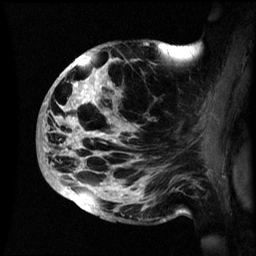
Breast MRI (dynamic contrast-enhanced), one sagittal slice; dynamic contrast-enhanced series, image 2 of 3 at this slice position (ordered by acquisition); 1.5 T; TE 4.2 ms, TR 8.4 ms; 256 × 256 image matrix, field of view 230 × 230 mm. Female patient, age 48 years.
Structures marked on this image (semi-automatically segmented with operator editing):
- analysis volume of interest (the breast-tissue region the enhancement analysis was run in; not a lesion): bounding box [x1, y1, x2, y2] px = [38, 41, 195, 222]
- tumour enhancement mask (voxels above the 70 % enhancement threshold inside the analysis volume of interest): [43, 56, 142, 213]